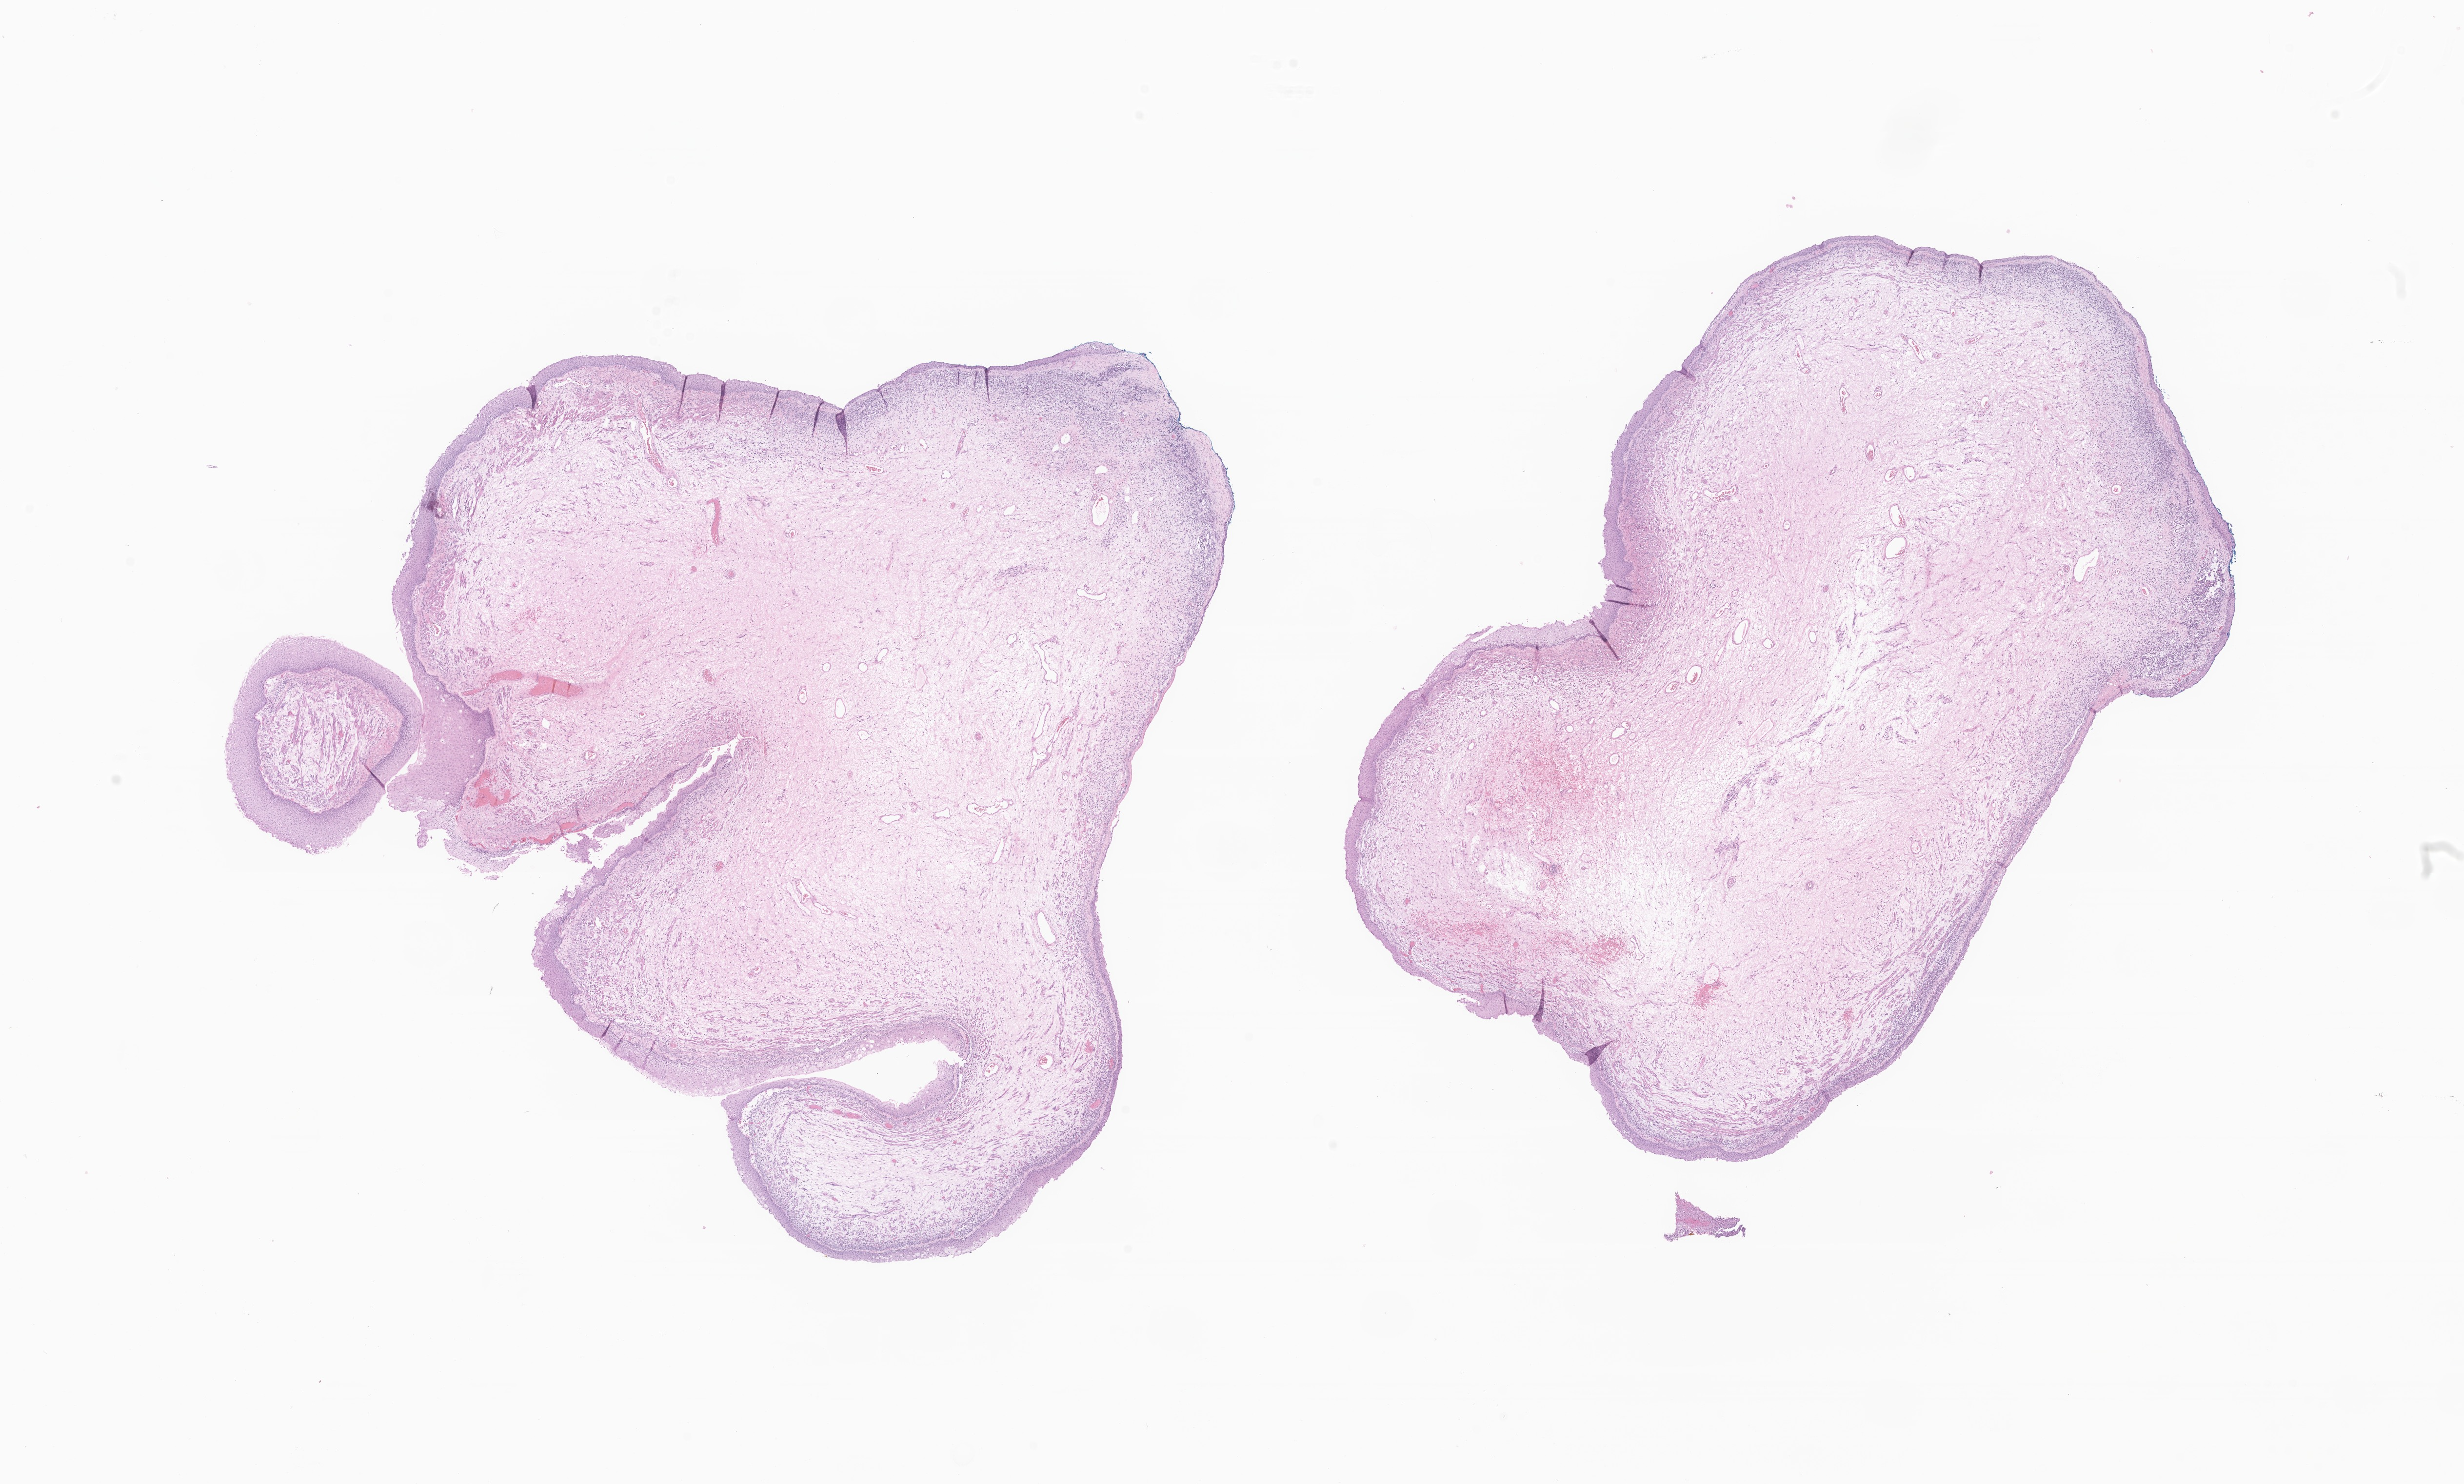
Whole-slide image, hematoxylin and eosin (H&E) stain of tumor tissue from the vagina, a low-resolution overview of the entire scanned area, about 21.3 x 12.8 mm; FFPE section. Female patient, age 644 days (about 1.8 years).
- recorded diagnosis: Embryonal rhabdomyosarcoma, NOS